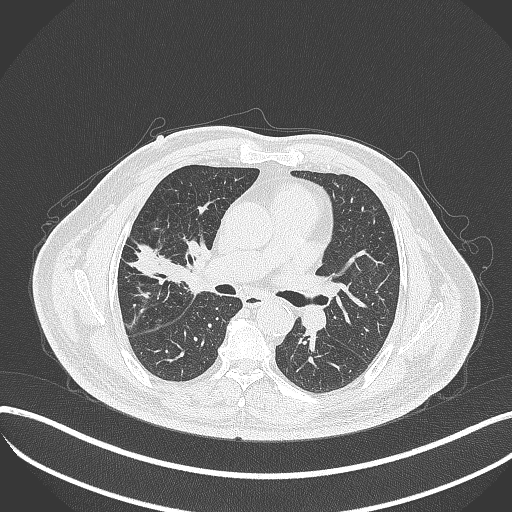
Chest CT, one axial slice. Slice 205 of 401 in the series (ordered by position). 120 kVp. Lung window (W 1500 / L -600 HU). 1 mm slice thickness. 512 × 512 image matrix. Male patient, age 72 years. From the clinical record (not read from this slice): clinical TNM (as recorded): T1c N0 M0.
Outlined on this slice (rectangle marked by the reading radiologist):
- lung tumour (recorded histology: squamous cell carcinoma): bounding box (x1, y1, x2, y2) in pixels: (176, 238, 209, 300)